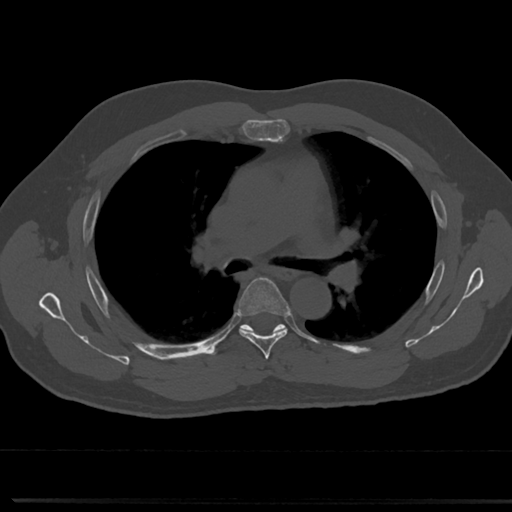
CT including the spine, one axial slice. Position 487 of 817 along the scan axis. Reconstruction kernel Br40s/3. 120 kVp. Bone window (W 1800 / L 400 HU). 0.5 mm slice thickness. 512 × 512 image matrix, field of view 355 × 355 mm. Patient: male, 61 years. Case-level facts recorded for this patient, not image findings: primary cancer: prostate.
Outlined on this slice (semi-automatically segmented with operator editing):
- T4 vertebra: bounding box <265,365,273,374> (left, top, right, bottom; pixels)
- T5 vertebra: <234,278,291,350>
- T6 vertebra: <243,327,282,329>